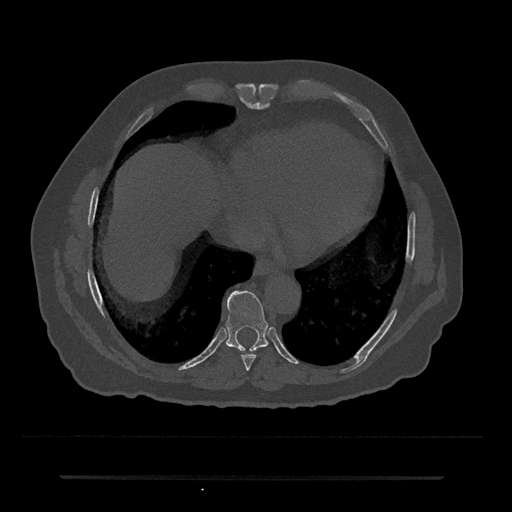
CT including the spine, one axial slice; slice 298 of 797 in the series (ordered by position); bone window (W 1800 / L 400 HU); 512 × 512 image matrix, field of view 437 × 437 mm. Patient: male, 69 years. From the clinical record (not read from this slice): primary cancer: prostate.
Annotated regions visible in this slice (semi-automatic segmentation, software-assisted and operator-edited):
- T8 vertebra: bounding box <241,354,256,371> (left, top, right, bottom; pixels)
- T9 vertebra: <226,290,268,351>